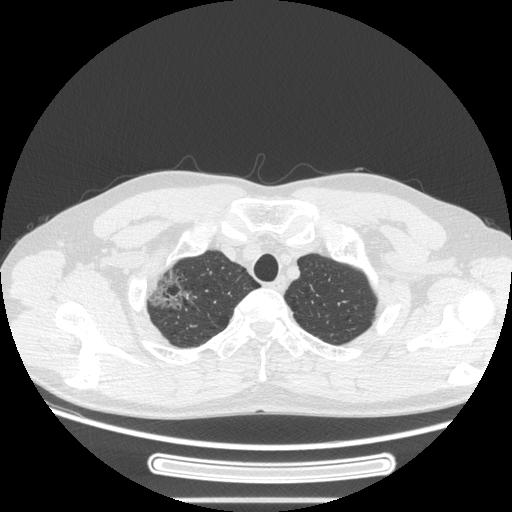
Chest CT, one axial slice. Slice 232 of 269 in the series (ordered by position). Lung window (W 1500 / L -600 HU). 1.25 mm slice thickness. 512 × 512 image matrix. Male patient, age 53 years. Case-level facts recorded for this patient, not image findings: clinical TNM (as recorded): T1c N0 M0; histopathological grade: G2.
Annotated regions visible in this slice (bounding box drawn by a radiologist):
- lung tumour (recorded histology: adenocarcinoma): bounding box [x1, y1, x2, y2] px = [139, 259, 195, 322]